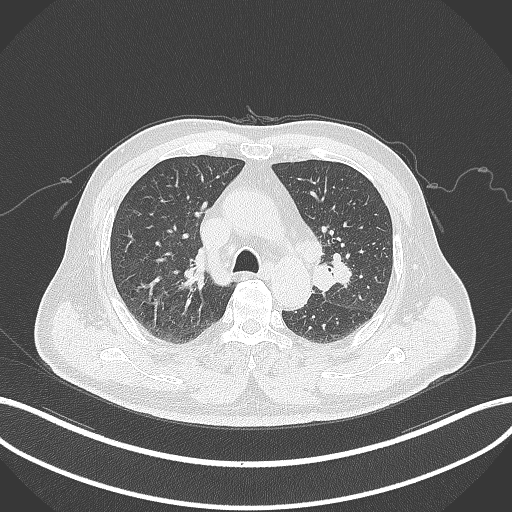
Chest CT, one axial slice; position 204 of 286 along the scan axis; lung window (W 1500 / L -600 HU); 512 × 512 image matrix, field of view 400 × 400 mm. Patient: male, 67 years. Case-level facts recorded for this patient, not image findings: clinical TNM (as recorded): T2a N1 M0; histopathological grade: G3.
Structures marked on this image (rectangle marked by the reading radiologist):
- lung tumour (recorded histology: adenocarcinoma): bounding box <313,254,356,294> (left, top, right, bottom; pixels)